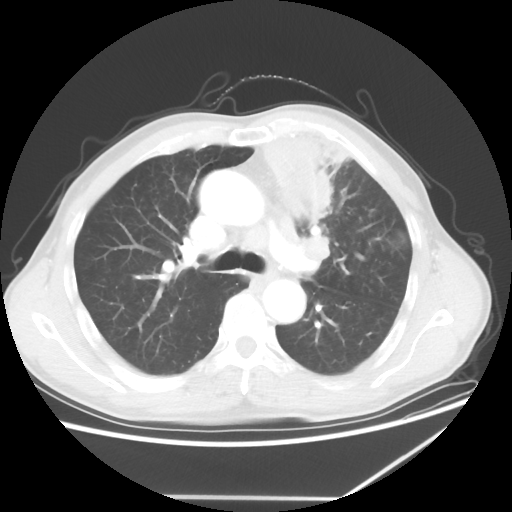
Chest CT, one axial slice. Slice 41 of 64 in the series (ordered by position). Reconstruction kernel STANDARD. Lung window (W 1500 / L -600 HU). 5 mm slice thickness. 512 × 512 image matrix, field of view 383 × 383 mm. Patient: male, 64 years. Case-level facts recorded for this patient, not image findings: clinical TNM (as recorded): T1c N1 M1; histopathological grade: G2.
Annotated regions visible in this slice (bounding box drawn by a radiologist):
- lung tumour (recorded histology: squamous cell carcinoma): box from (x=263, y=130) to (x=356, y=217) px